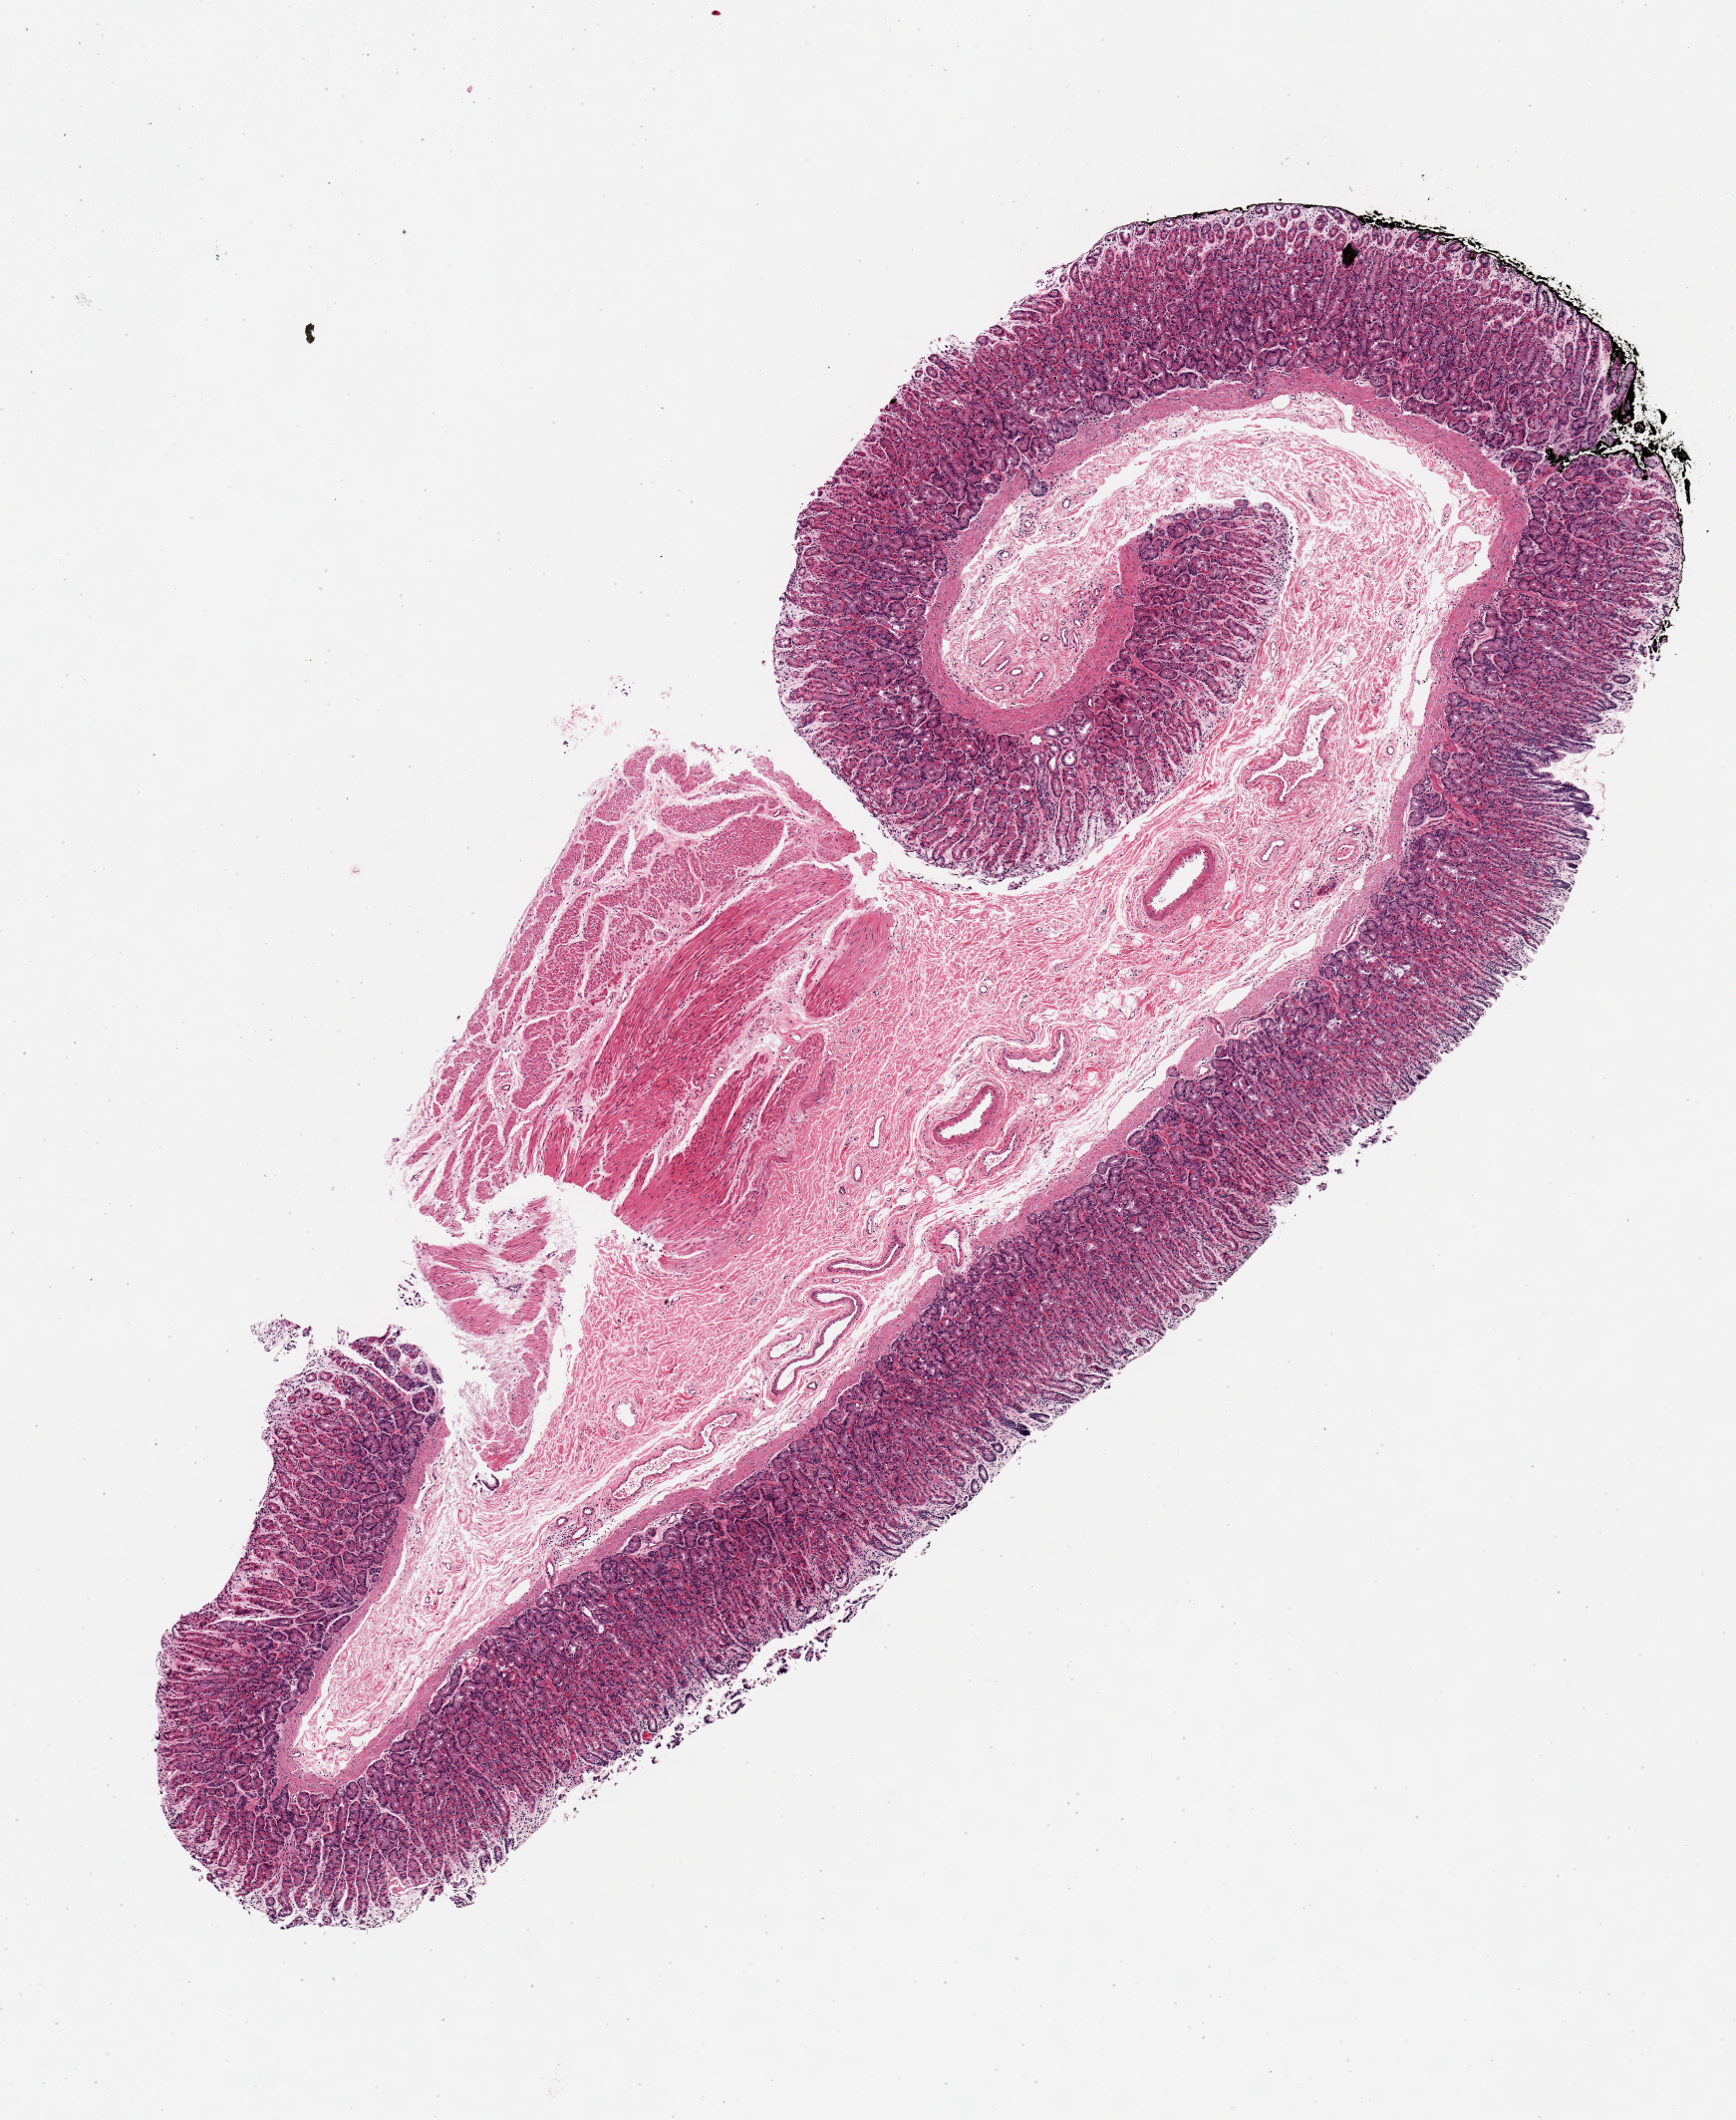
Haematoxylin and eosin whole-slide image — low-resolution overview of the scanned area, about 6.9 x 8.4 mm. Female donor.
Specimen: PAXgene-fixed, paraffin-embedded tissue; target tissue: stomach; tissue donor sample.